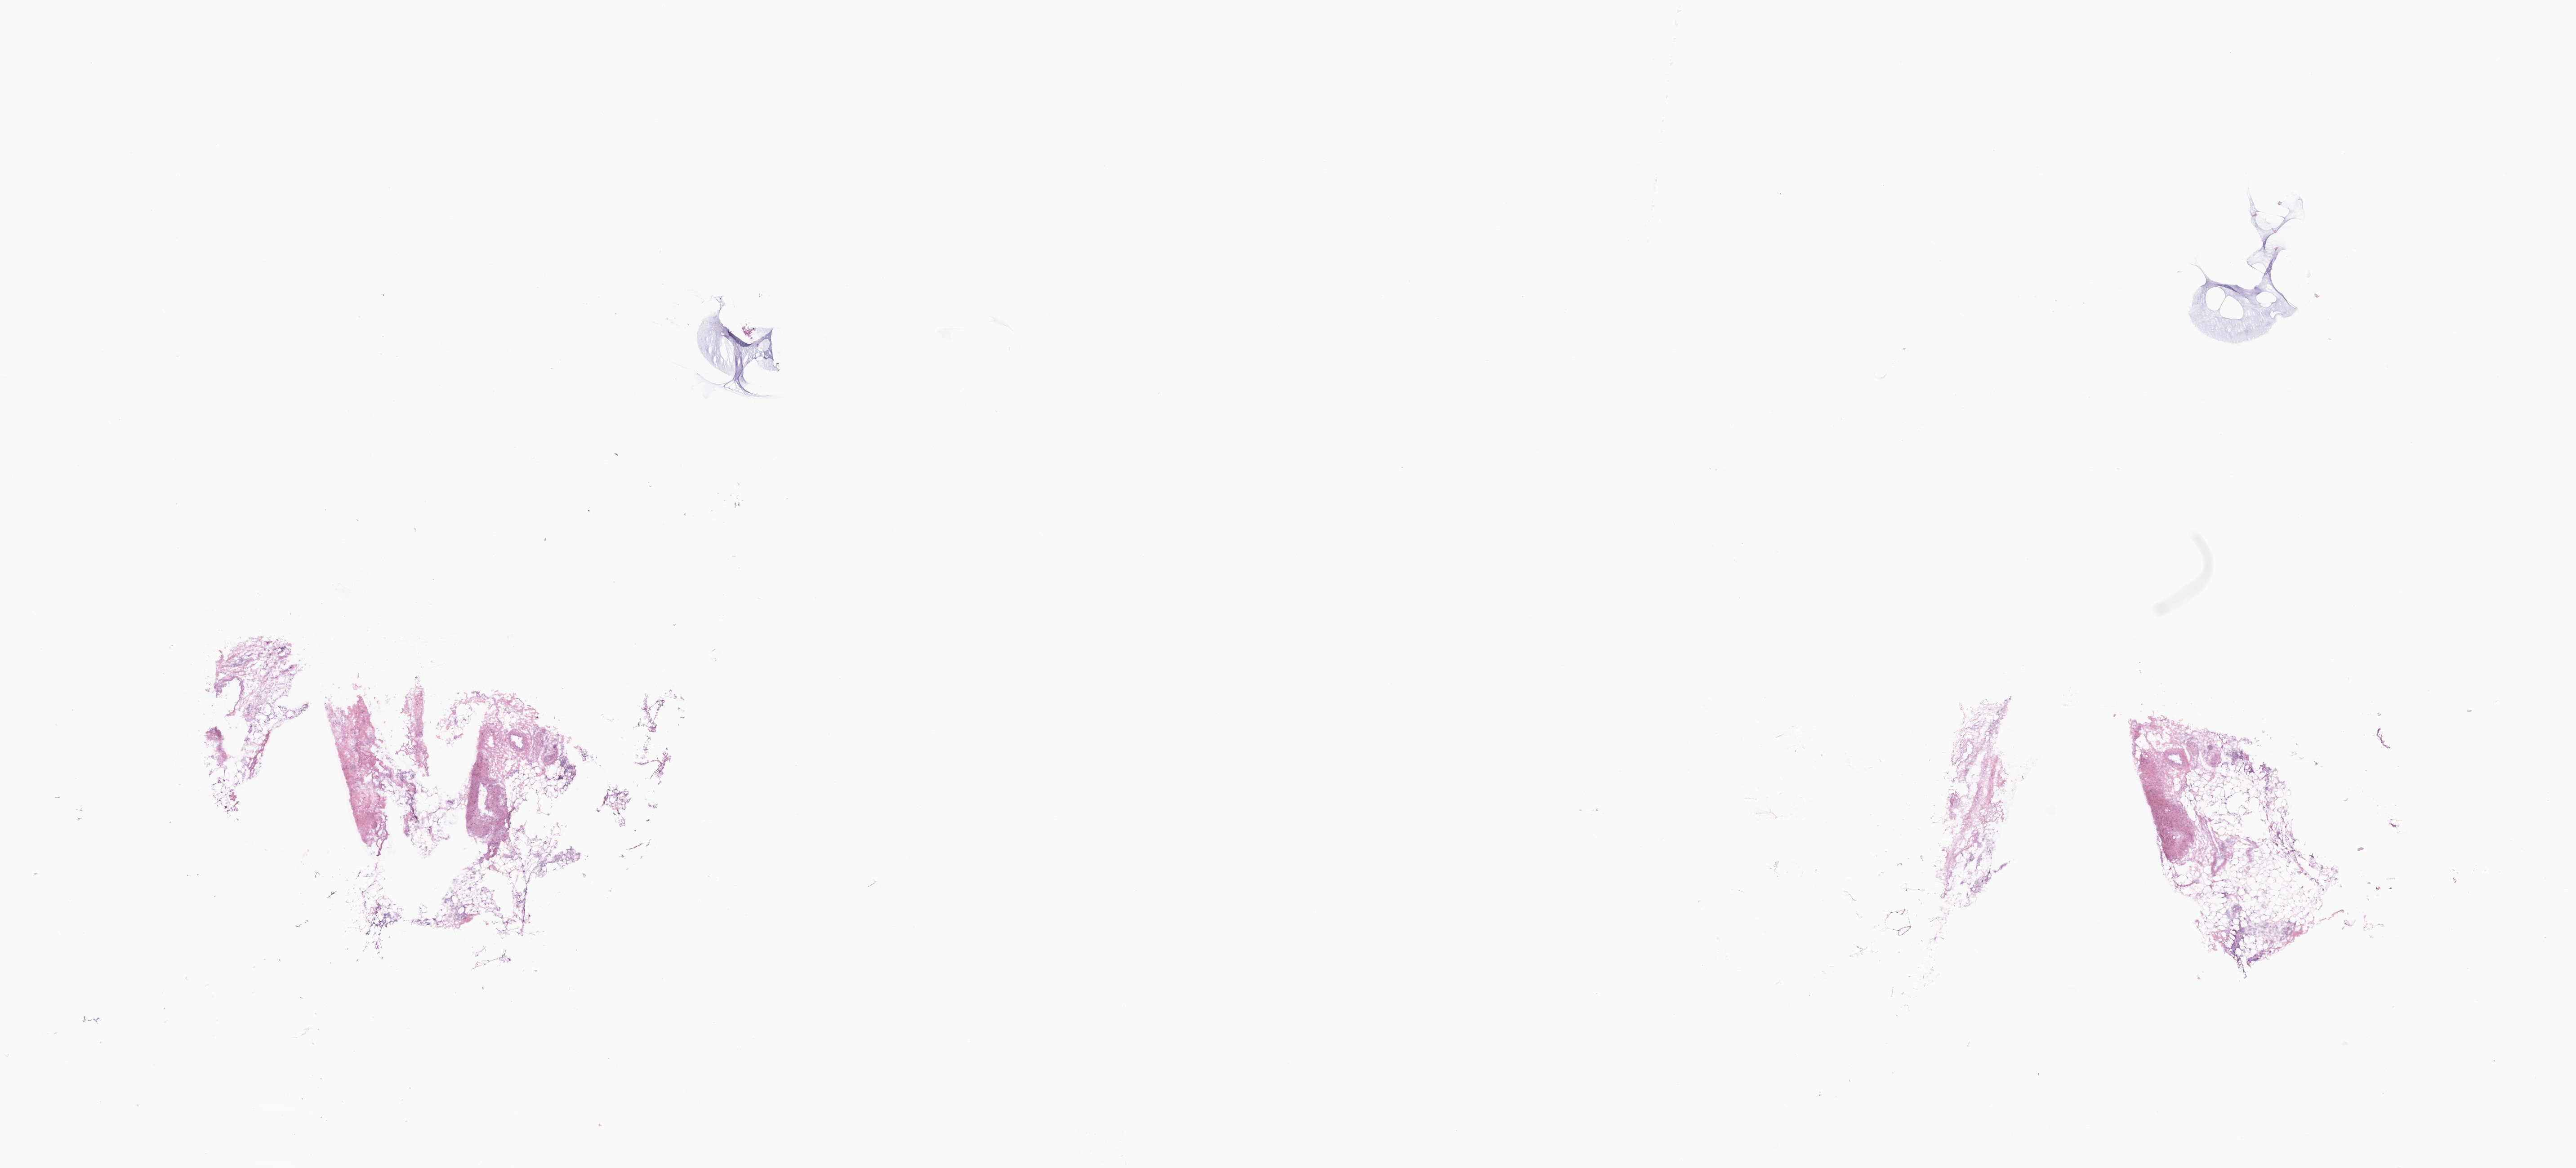
Digitized H&E-stained section, shown as a low-resolution overview of the whole scanned area (about 24.2 x 11.0 mm); frozen section (tissue freezing medium); specimen: primary tumor; site: breast (left). Patient: female, age at initial diagnosis 69 years. Pathologist review of this section (percent, as recorded): tumor cells 10%, tumor nuclei 40%, stromal cells 90%, necrosis 0%, normal cells 0%. Infiltration values recorded for this section: lymphocyte infiltration 0%, monocyte infiltration 0%, neutrophil infiltration 0%.
Section: bottom of the tissue portion. Histologic diagnosis: Infiltrating duct carcinoma, NOS.